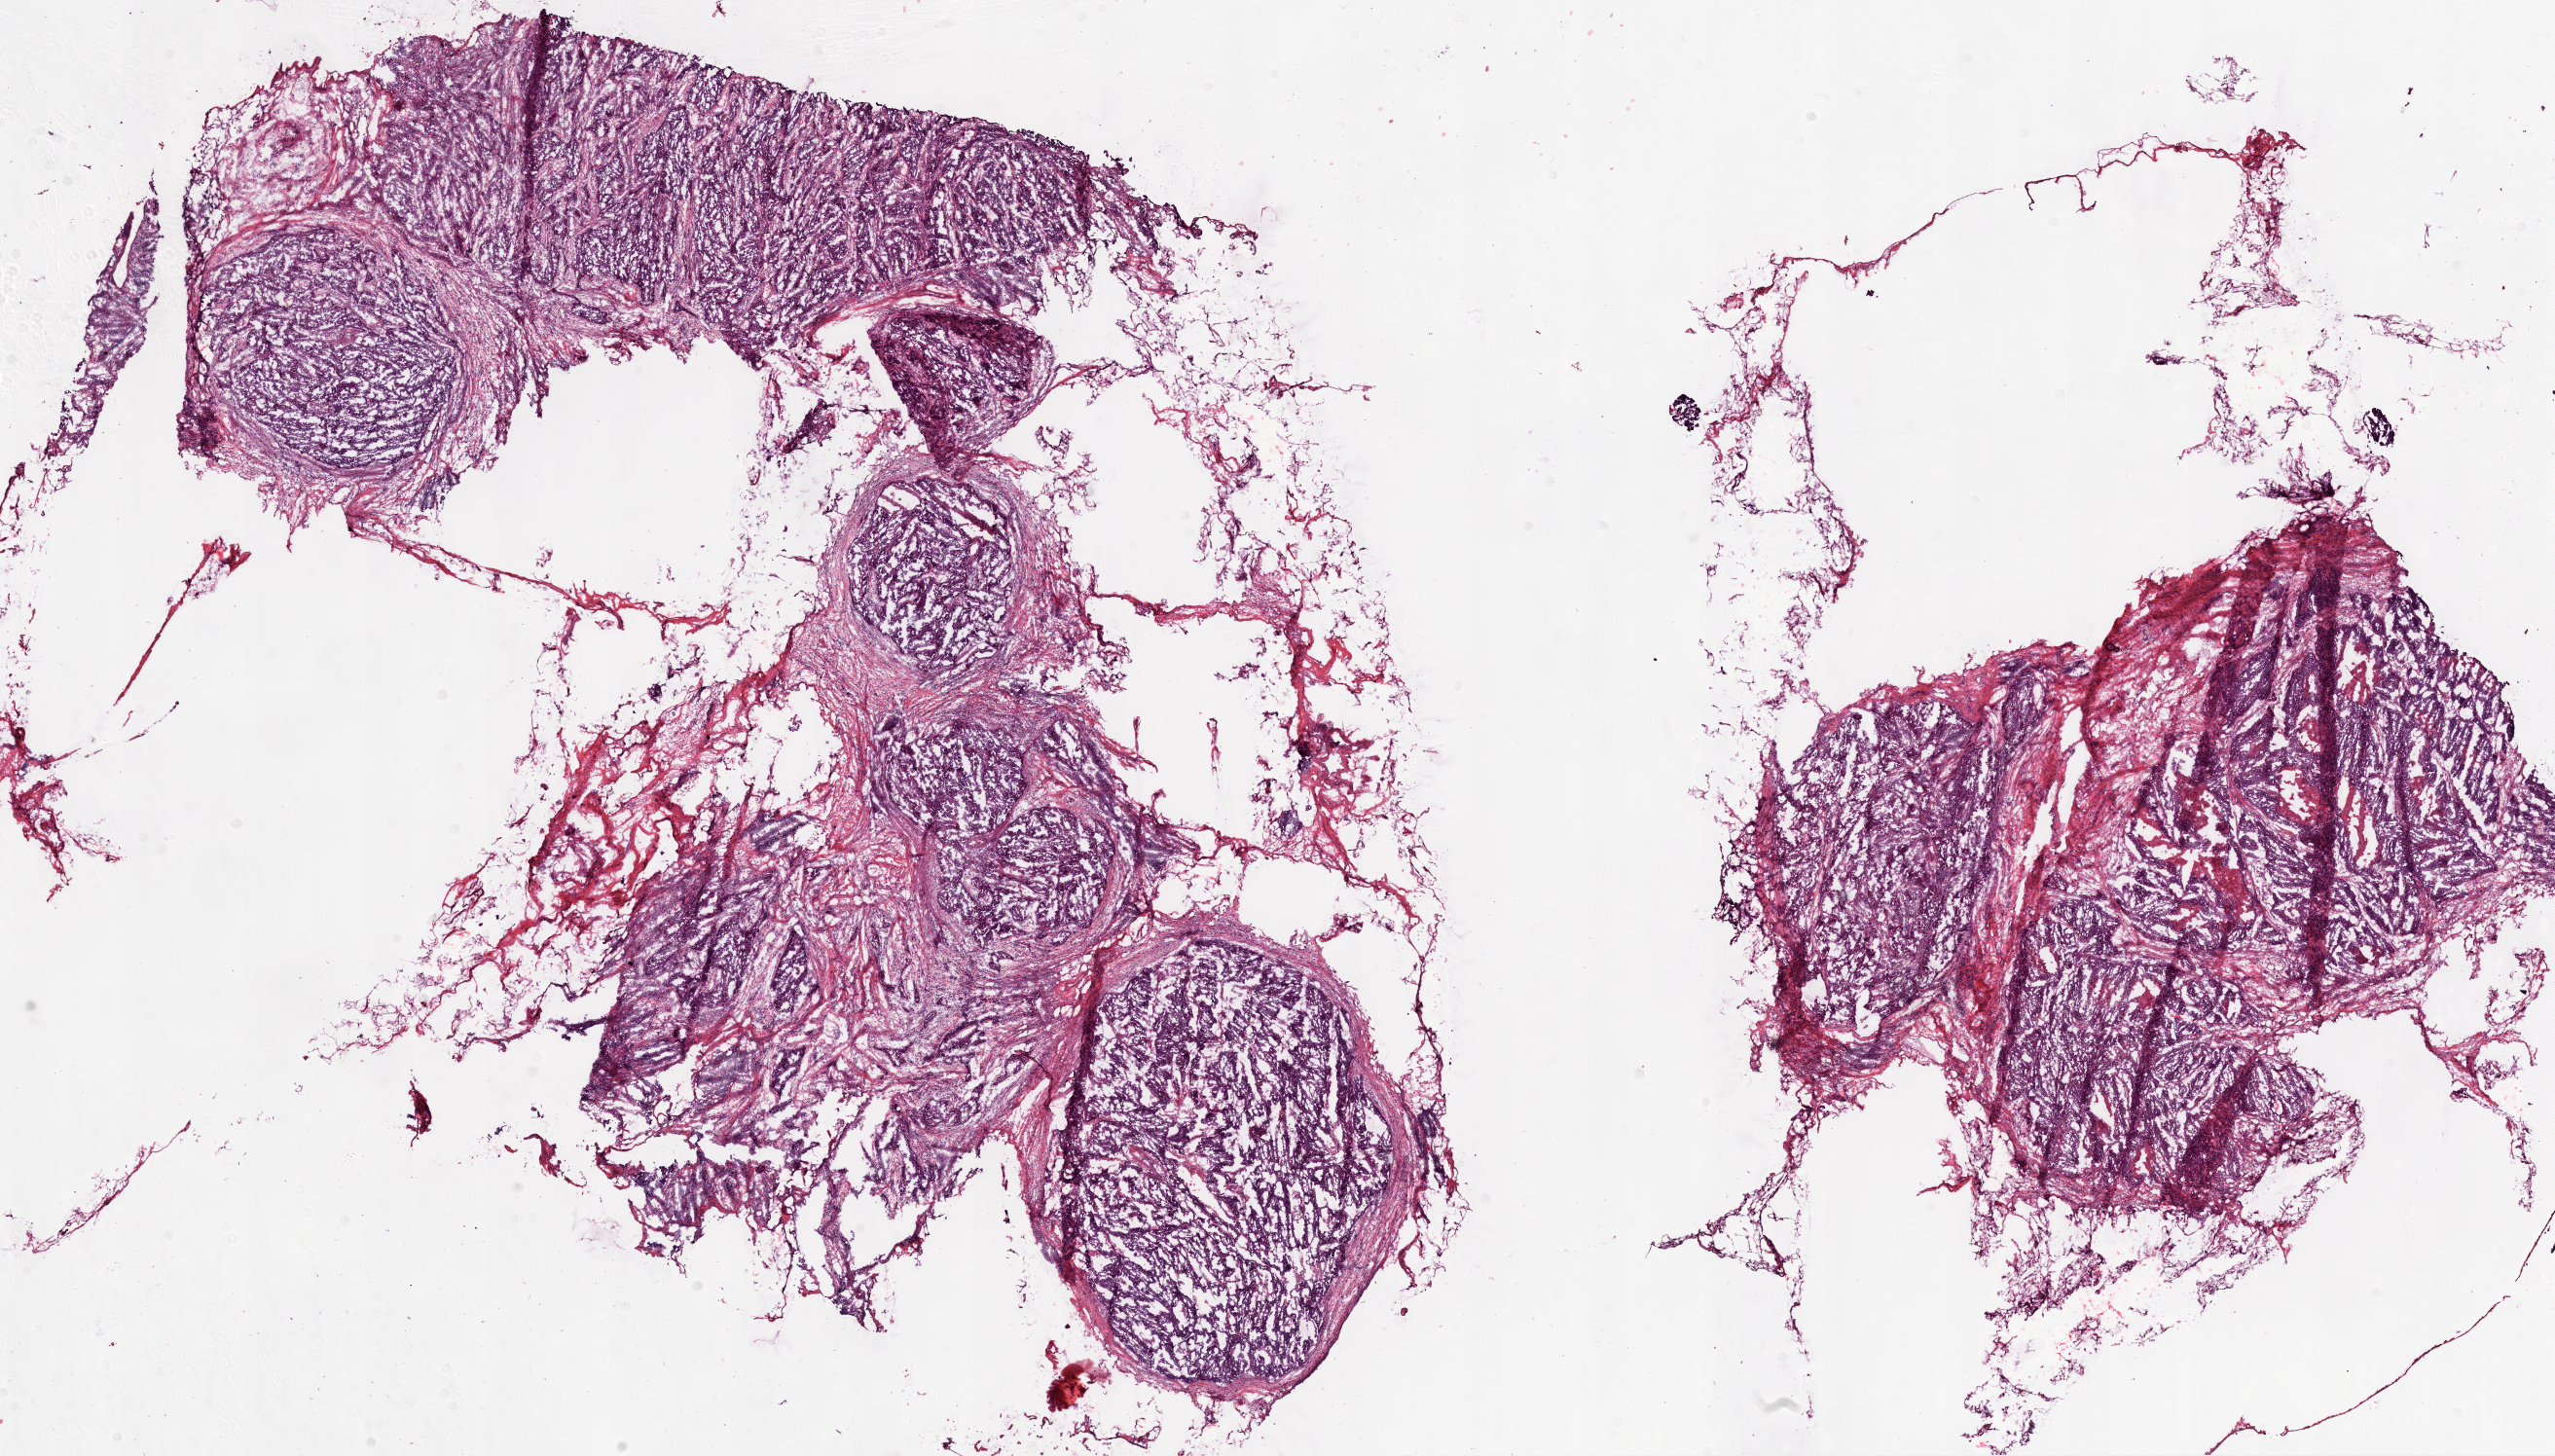
Whole-slide histology image, H&E-stained, a low-resolution overview of the entire scanned area, about 21.1 x 12.0 mm (slide scanned at 20x). Frozen section from the bottom of the tissue portion. Primary tumour sample from the ovary. Female patient; age at initial diagnosis 59 years. Composition of this section per pathologist review: tumour cells 70%, tumour nuclei 85%.
Histologic diagnosis: Serous cystadenocarcinoma, NOS.